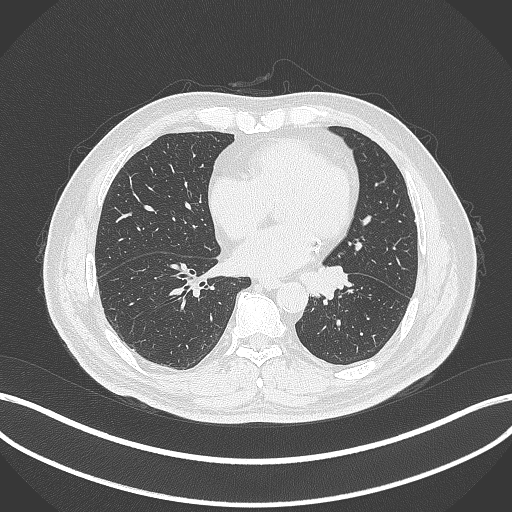
Chest CT, one axial slice; position 111 of 312 along the scan axis; lung window (W 1500 / L -600 HU); 1 mm slice thickness; 512 × 512 image matrix. Male patient, age 71 years. From the clinical record (not read from this slice): clinical TNM (as recorded): T1b N0 M0.
Annotated regions visible in this slice (rectangle marked by the reading radiologist):
- lung tumour (recorded histology: squamous cell carcinoma): bounding box (x1, y1, x2, y2) in pixels: (300, 263, 353, 304)